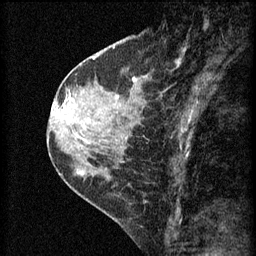
Breast MRI (dynamic contrast-enhanced), one sagittal slice; slice 24 of 60 in the series (ordered by position); 3 images stored at this slice position (order not interpretable as contrast timing); 1.5 T; TE 4.2 ms, TR 8.2 ms; 256 × 256 image matrix, field of view 180 × 180 mm. Patient: female, 45 years.
Outlined on this slice (semi-automatically segmented with operator editing):
- analysis volume of interest (the breast-tissue region the enhancement analysis was run in; not a lesion): bounding box <62,98,104,139> (left, top, right, bottom; pixels)
- tumour enhancement mask (voxels above the 70 % enhancement threshold inside the analysis volume of interest): <64,98,74,109>